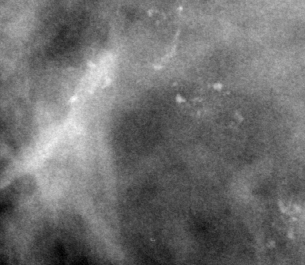
Cropped region of a digitized screen-film mammogram centred on a radiologist-marked abnormality, right breast, CC view.
Calcifications, morphology pleomorphic, distribution linear; BI-RADS assessment category 5; pathology result (as recorded, not read from the image): malignant.